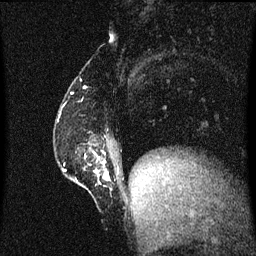
Breast MRI (dynamic contrast-enhanced), one sagittal slice; position 15 of 60 along the scan axis; dynamic contrast-enhanced series, image 2 of 3 at this slice position (ordered by acquisition); 1.5 T; TE 4.2 ms, TR 8.4 ms; 256 × 256 image matrix, field of view 200 × 200 mm. Female patient, age 52 years. From the clinical record (not read from this slice): setting: breast cancer imaged before/during neoadjuvant chemotherapy; receptor status: HER2-positive.
Outlined on this slice (semi-automatic segmentation, software-assisted and operator-edited):
- analysis volume of interest (the breast-tissue region the enhancement analysis was run in; not a lesion): bounding box [x1, y1, x2, y2] px = [63, 144, 113, 193]
- tumour enhancement mask (voxels above the 70 % enhancement threshold inside the analysis volume of interest): [97, 162, 110, 181]